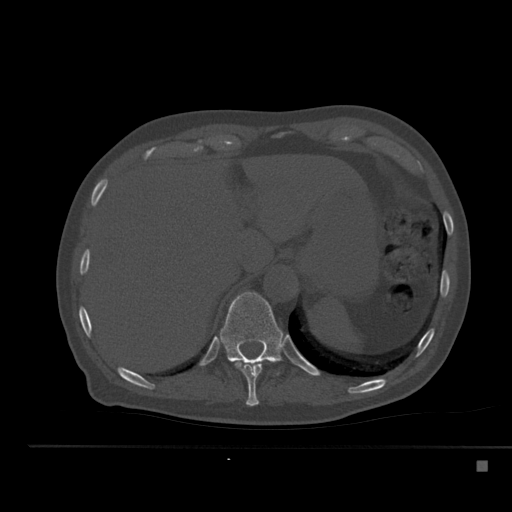
CT including the spine, one axial slice; reconstruction kernel Br40s; 120 kVp; bone window (W 1800 / L 400 HU); 1.5 mm slice thickness; 512 × 512 image matrix, field of view 408 × 408 mm. Patient: male, 70 years. Case-level facts recorded for this patient, not image findings: primary cancer: renal; vertebrae with lytic lesions (as recorded): T4, T6, T10, T12, L3, L4, L5.
Annotated regions visible in this slice (semi-automatic segmentation, software-assisted and operator-edited):
- T10 vertebra: bounding box (x1, y1, x2, y2) in pixels: (235, 359, 269, 406)
- T11 vertebra: (217, 292, 286, 374)